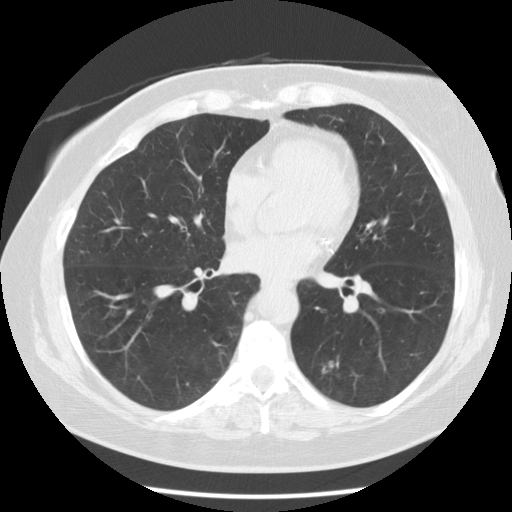
Low-dose screening chest CT, axial slice; second screening round (one year after baseline); lung window (W 1500 / L -600 HU); 2.5 mm slice thickness; 512 × 512 image matrix. Female, age 59 years at enrolment. Current smoker at enrolment.
Expert reader's lesion annotation, bounding box [x1, y1, x2, y2] px = [299, 340, 367, 407]. The screening reader recorded 5 non-calcified nodules or masses ≥4 mm on this exam (right upper lobe, right lower lobe, right lower lobe, left lower lobe, left lower lobe); which of them this box marks is not recorded. Participant outcome: lung cancer diagnosed 343 days after this screen — adenocarcinoma, NOS, left lower lobe, poorly differentiated (G3), stage IA (AJCC 6th edition), 15 mm at pathology.